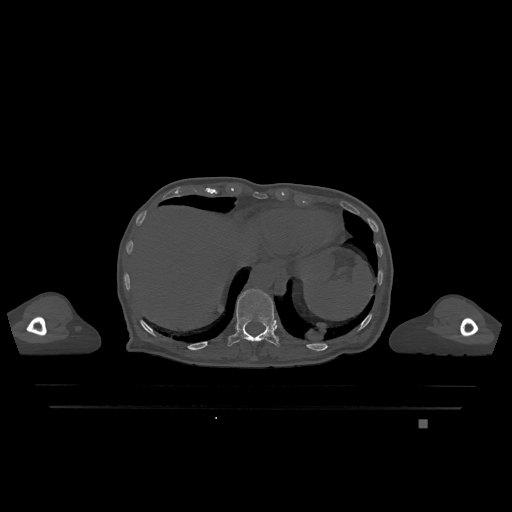
CT including the spine, one axial slice. Slice 593 of 1317 in the series (ordered by position). Bone window (W 1800 / L 400 HU). 0.5 mm slice thickness. 512 × 512 image matrix, field of view 500 × 500 mm. Female patient, age 74 years. From the clinical record (not read from this slice): primary cancer: lung.
Structures marked on this image (semi-automatic segmentation, software-assisted and operator-edited):
- T11 vertebra: bounding box (x1, y1, x2, y2) in pixels: (228, 289, 280, 347)